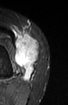
MRI of an extremity soft-tissue mass, one axial slice; position 25 of 52 along the scan axis; STIR; MR volume resampled by the dataset authors to the PET/CT grid (not the native acquisition matrix); 68 × 105 image matrix, field of view 66 × 103 mm. Female patient. From the clinical record (not read from this slice): histological type: spindle cell suggestive of biphasic synovial sarcoma; grade: intermediate; site of the primary tumour: left knee.
Annotated regions visible in this slice (expert contour drawn on MRI and transferred to this co-registered scan by the dataset authors):
- gross tumour volume including surrounding oedema: bounding box (x1, y1, x2, y2) in pixels: (14, 32, 38, 81)
- gross tumour volume (mass): (14, 34, 38, 81)